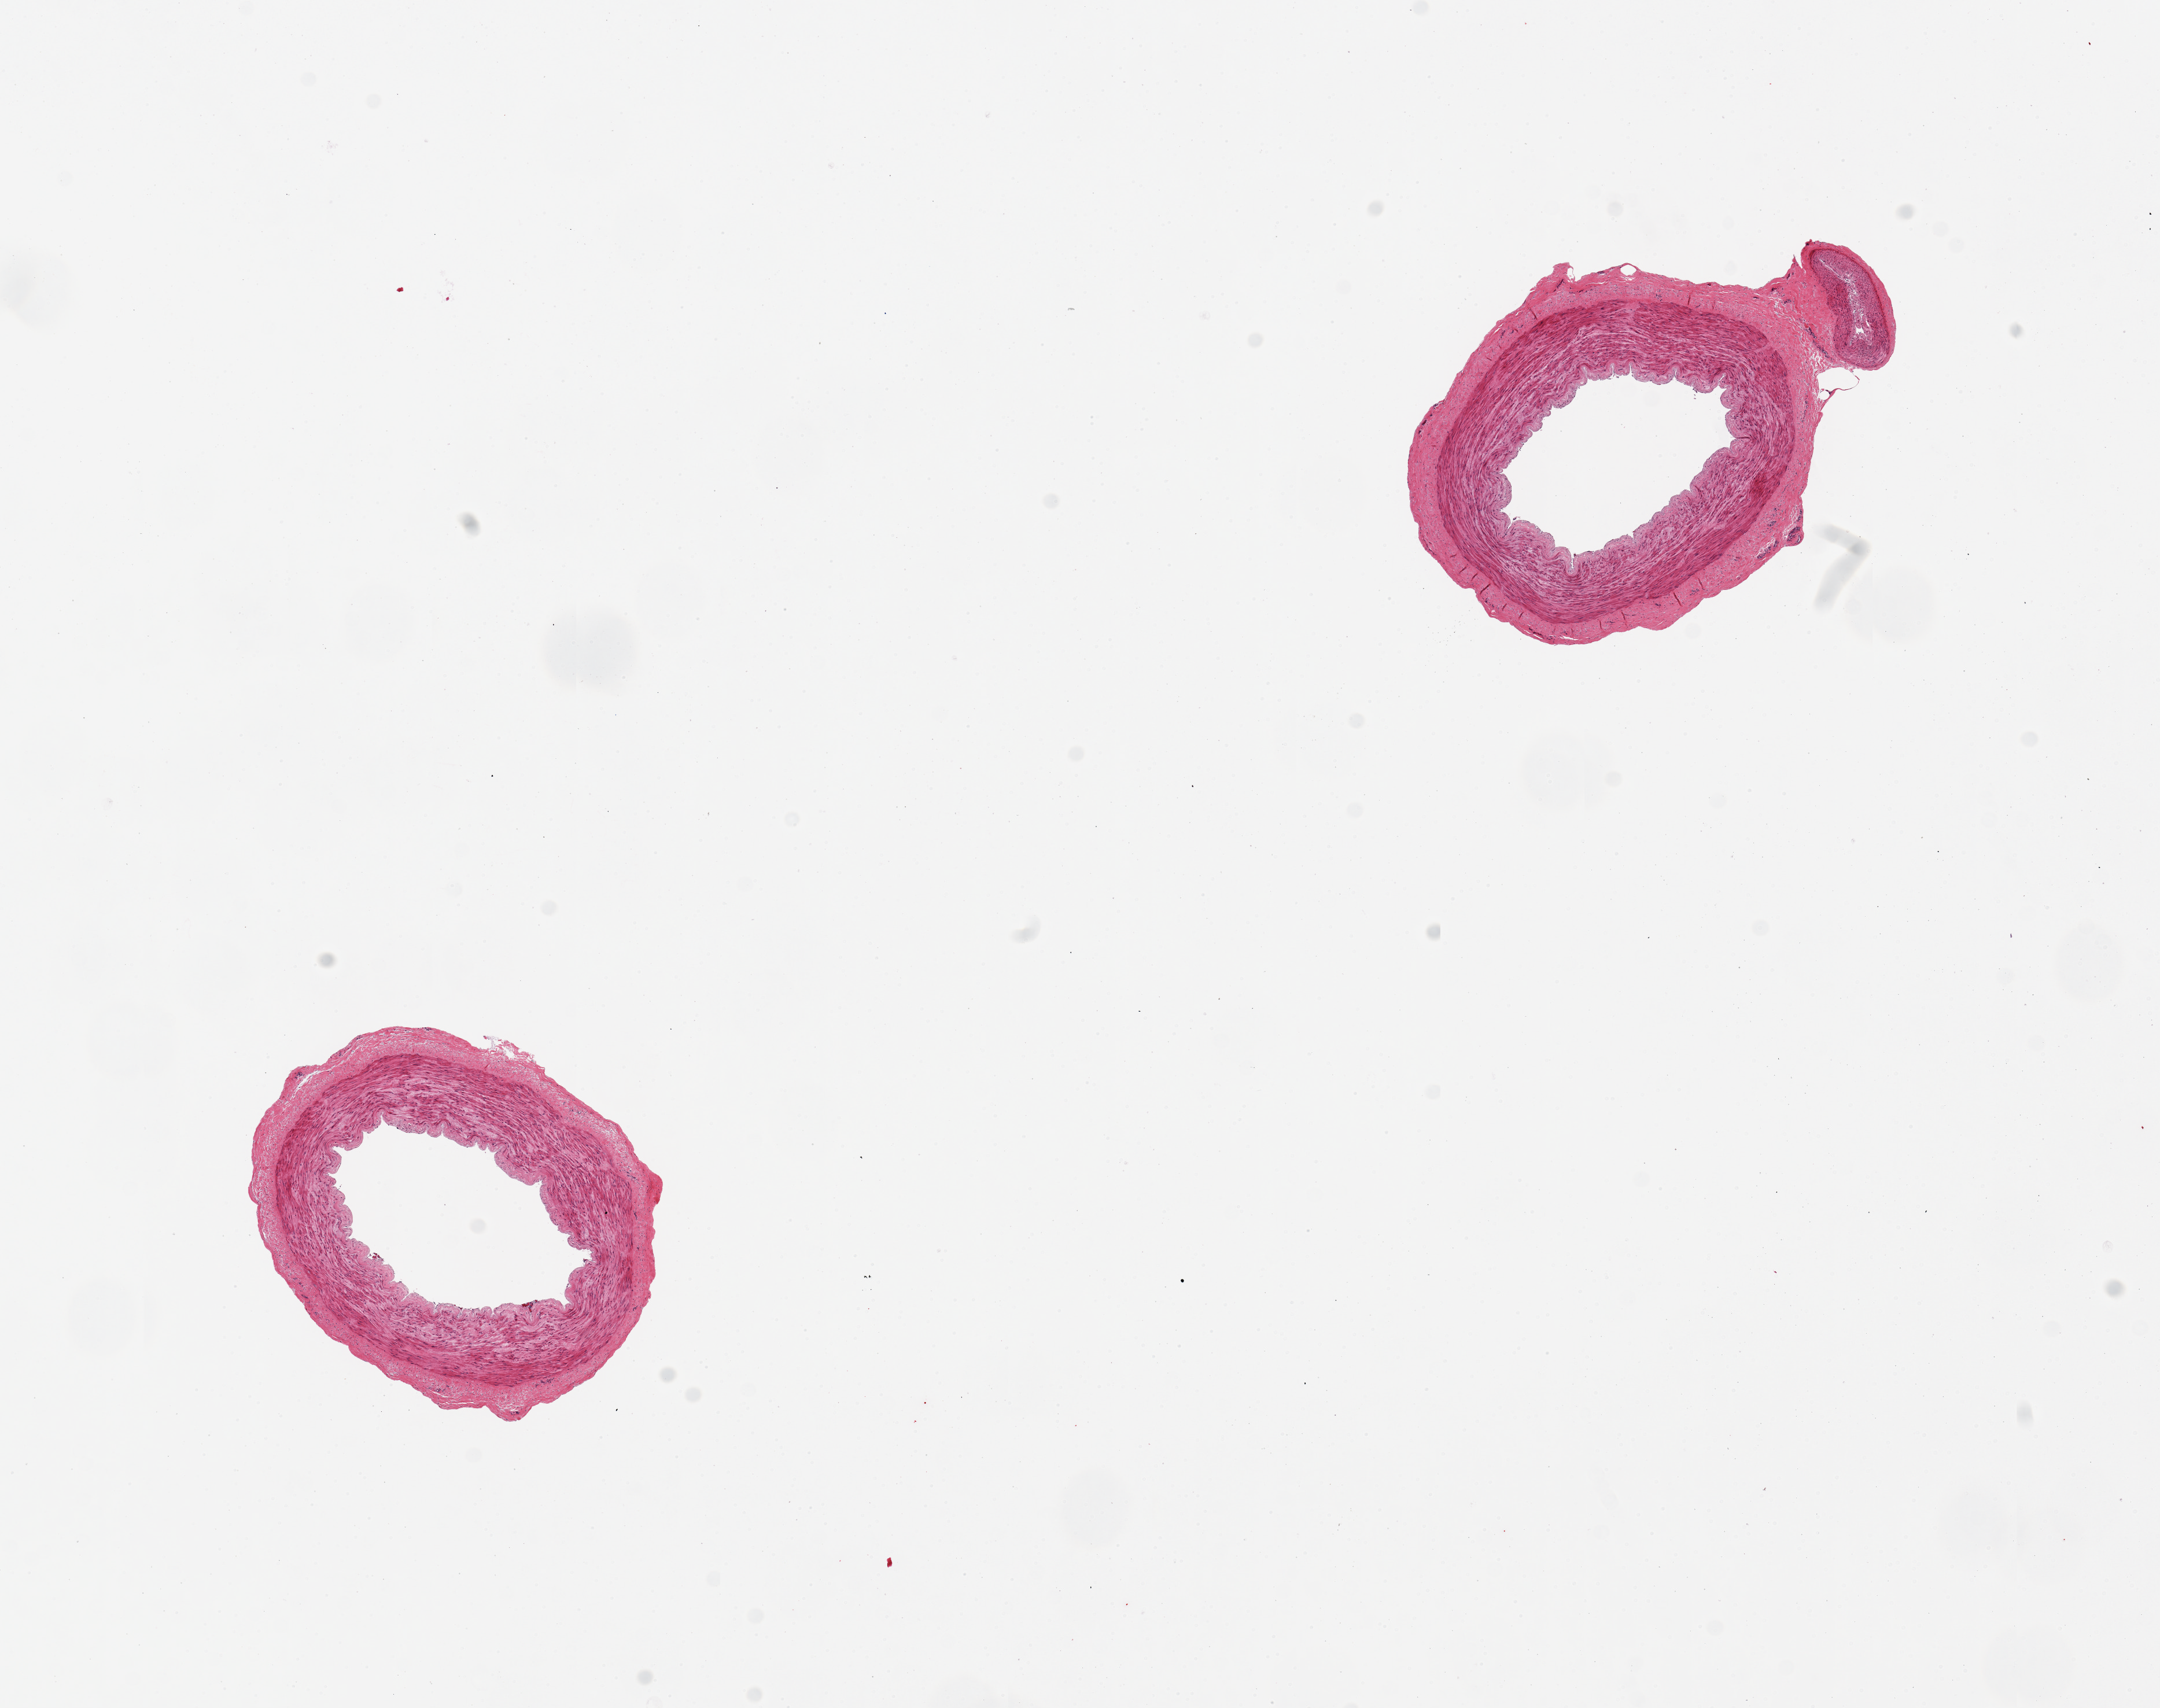
Digitized haematoxylin and eosin-stained section — whole scanned area (about 14.8 x 11.7 mm) shown as a low-resolution overview; PAXgene-fixed paraffin-embedded (PFPE) section; target tissue: tibial artery; donor tissue sample. Donor: male.
Review note (as recorded): 2 pieces, good clean specimens.